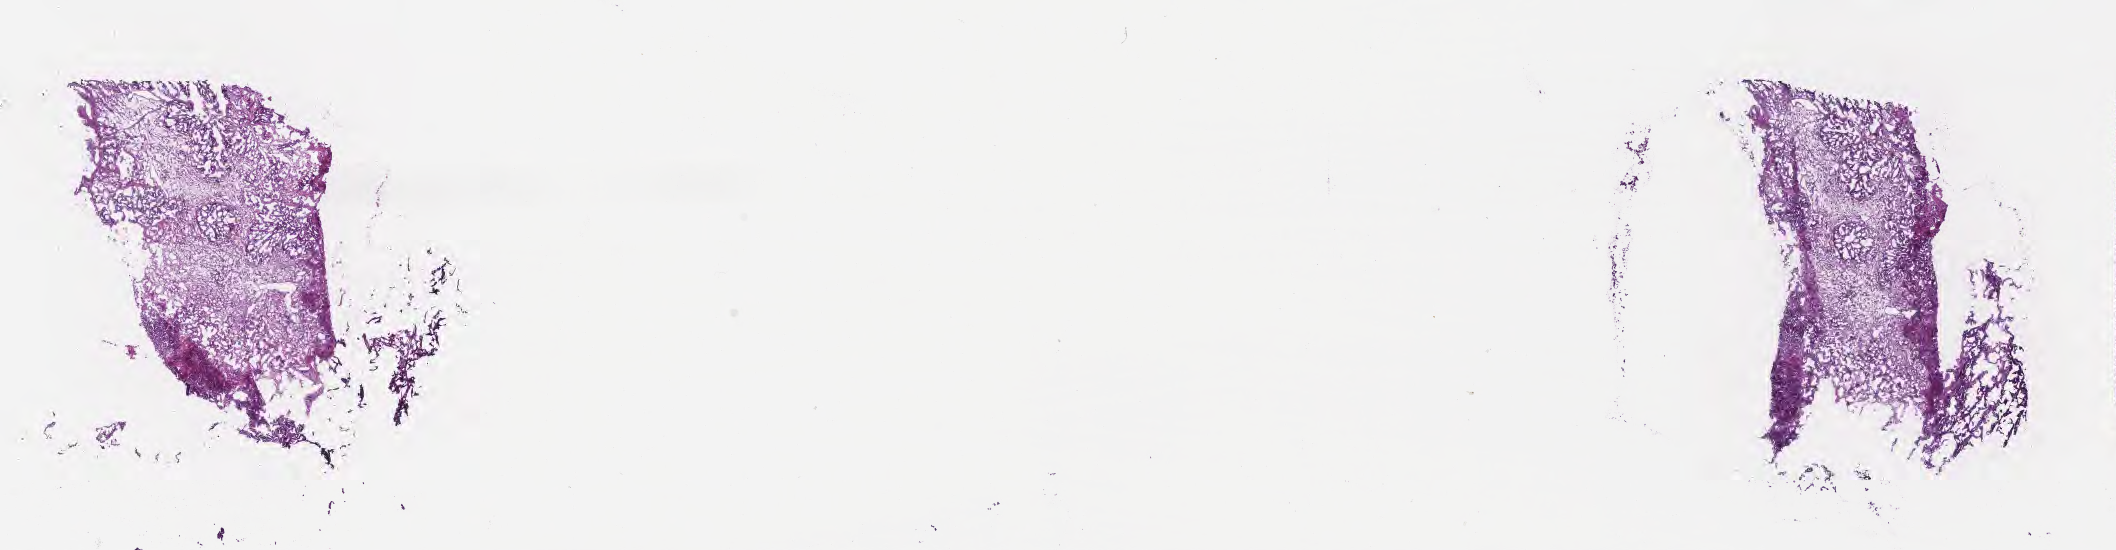
Haematoxylin and eosin whole-slide image — low-resolution overview of the scanned area, about 17.1 x 4.4 mm; frozen section; specimen: primary tumor; site: stomach. Patient: male, age at initial diagnosis 43 years. Slide review estimates, as recorded: tumor cells 100%, tumor nuclei 35%, stromal cells 0%, necrosis 0%, normal cells 0%. Infiltration values recorded for this section: lymphocyte infiltration 0%, monocyte infiltration 0%, neutrophil infiltration 0%.
Histologic diagnosis: Adenocarcinoma, NOS.